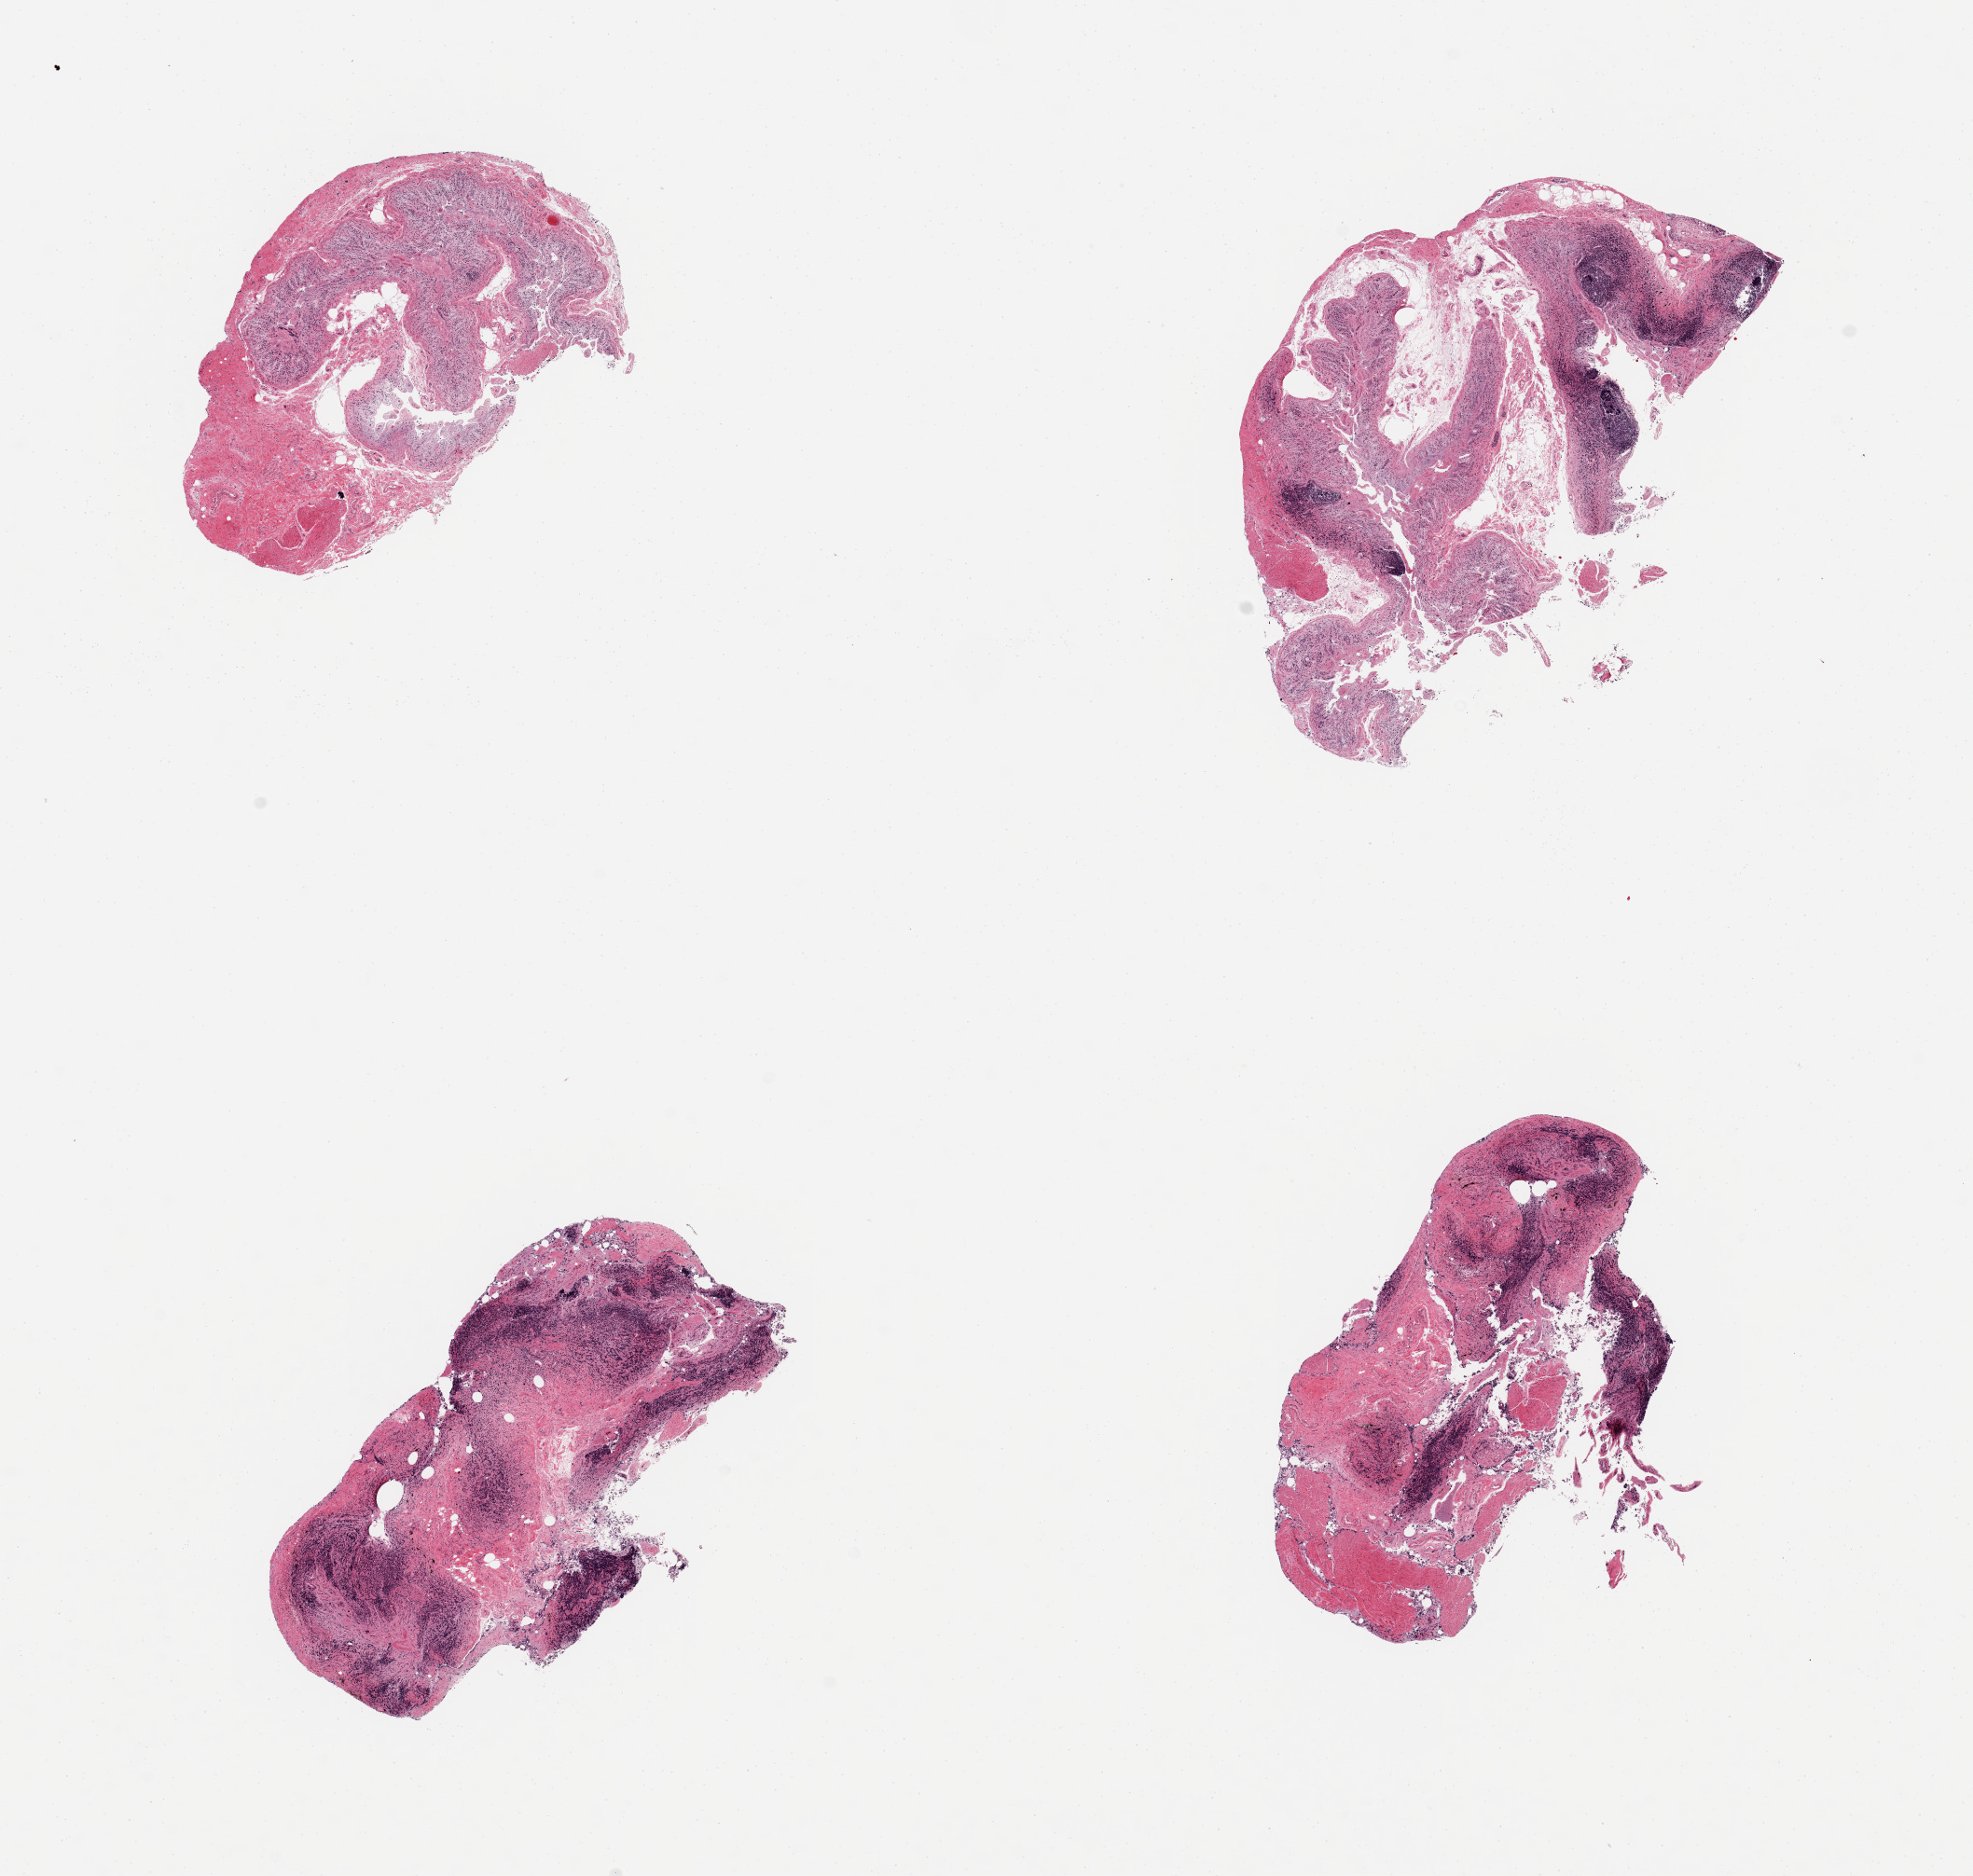
Whole-slide image, haematoxylin and eosin stain — whole scanned area (about 16.7 x 15.9 mm) shown as a low-resolution overview, PAXgene-fixed paraffin-embedded (PFPE) section, target tissue: ileum, tissue donor sample. Donor sex: male.
Reviewer comment on this tissue sample: 4 pieces, predominantly autolyzed mucosa with residual lymphoid nodules (some) and muscularis.